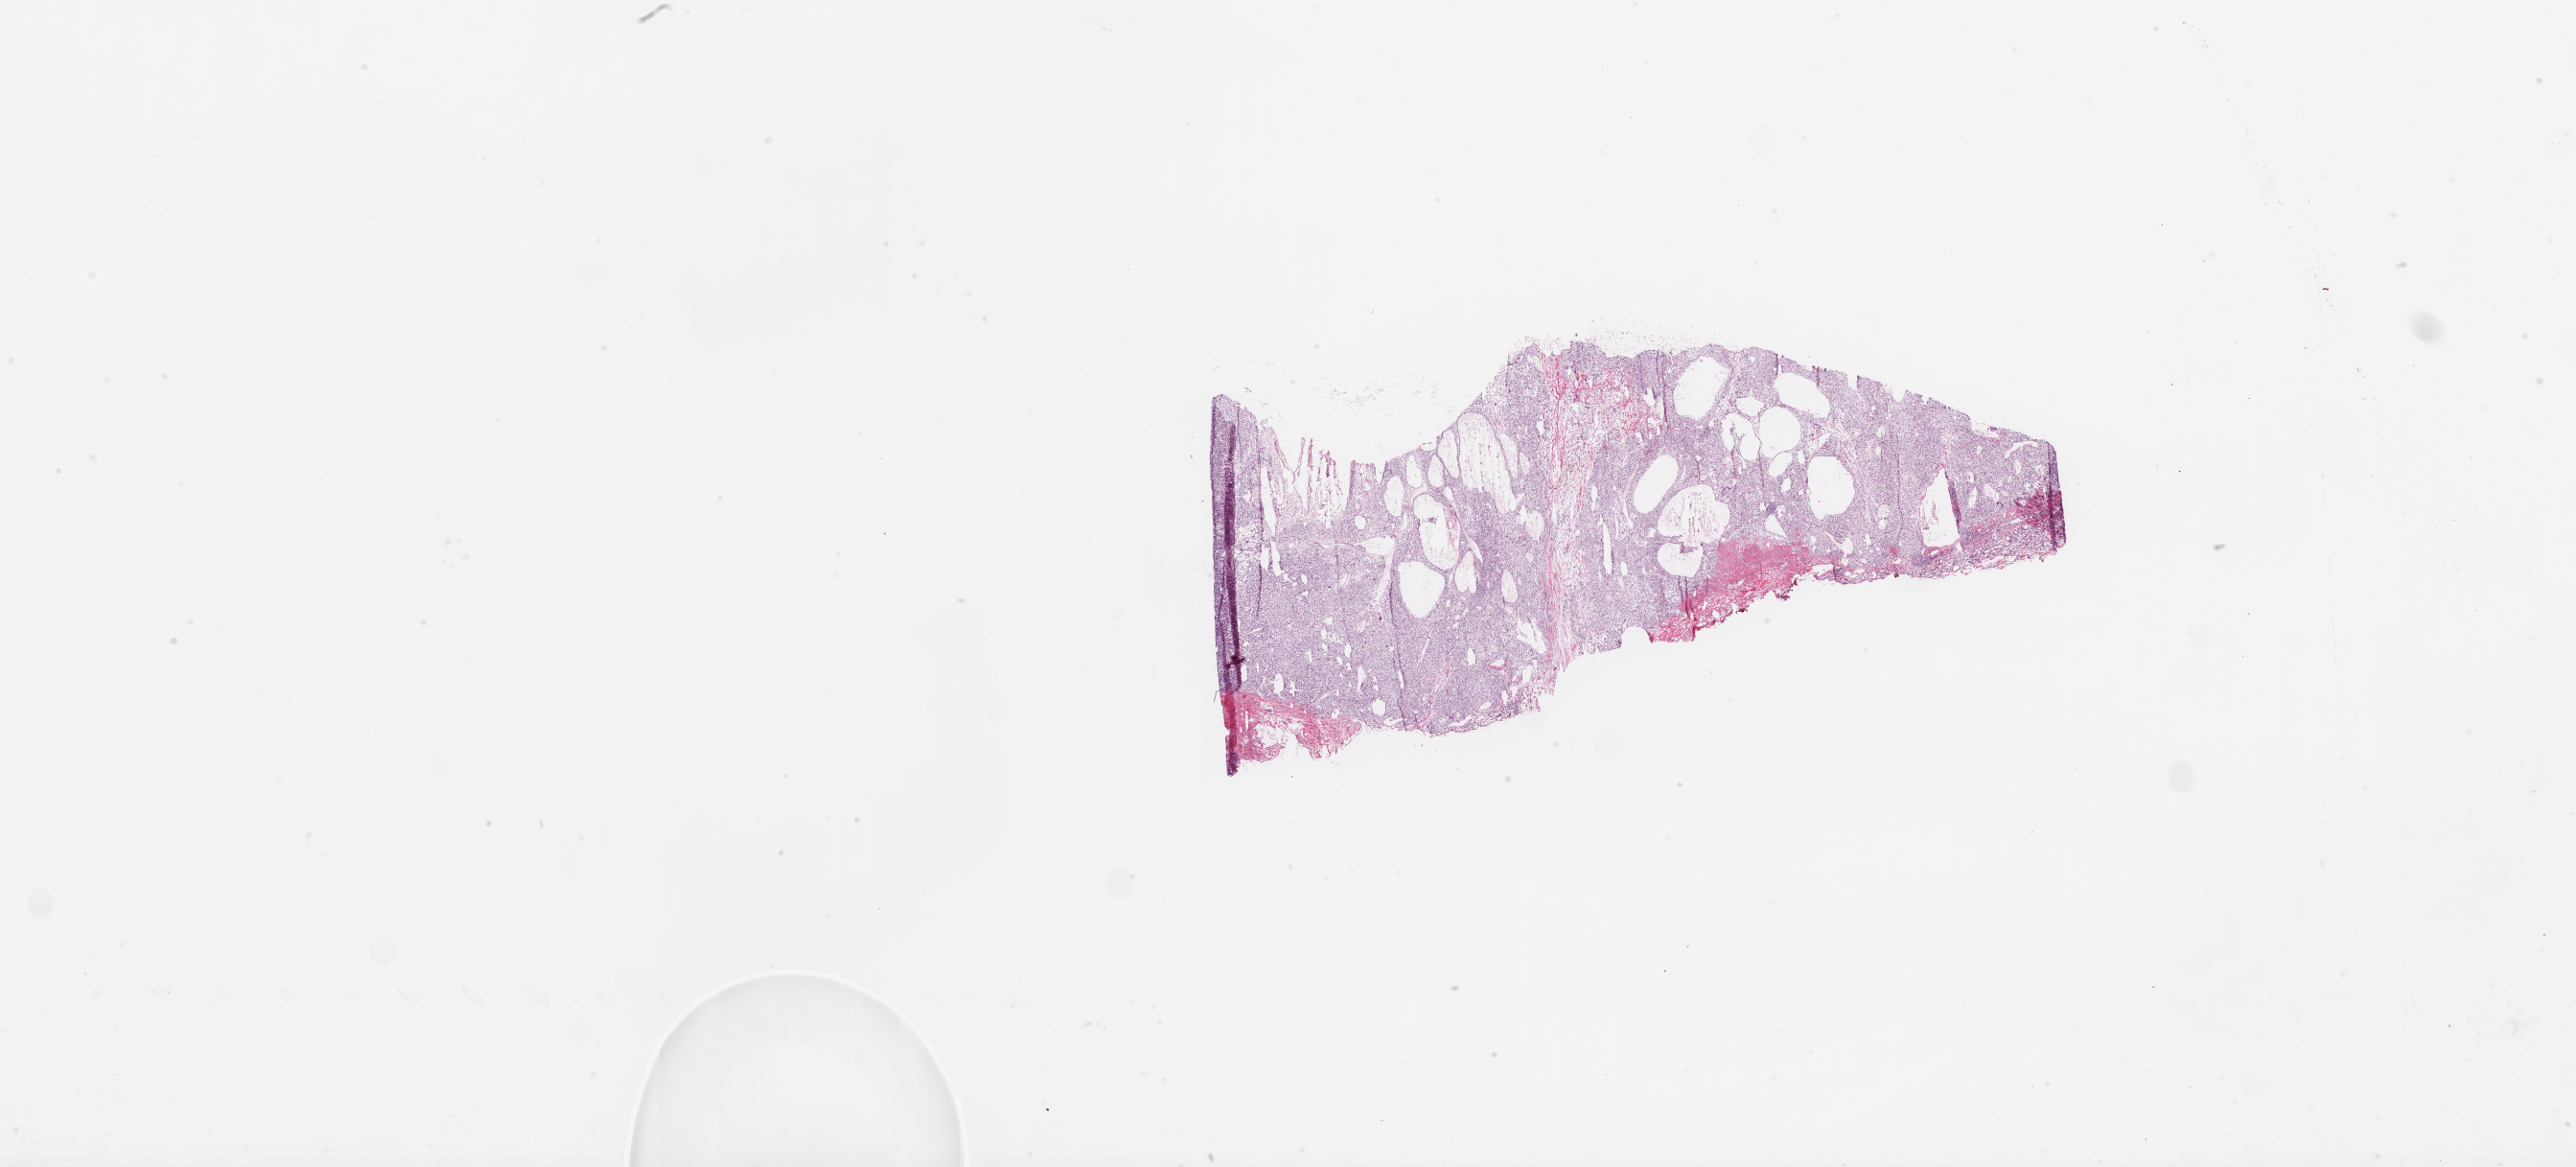
Digitized H&E-stained tissue section (whole slide) — a low-resolution overview of the entire scanned area, about 43.1 x 19.5 mm, frozen section, kidney, primary tumour sample. Male, age 46 years at initial diagnosis. Histologic grade: G2 (moderately differentiated). Slide review estimates, as recorded: tumour cells 85%, tumour nuclei 85%, normal cells 10%, stromal cells 5%, necrosis 0%.
• laterality: right
• diagnosis: Clear cell adenocarcinoma, NOS
• TNM: T1a NX M0
• AJCC pathologic stage: I